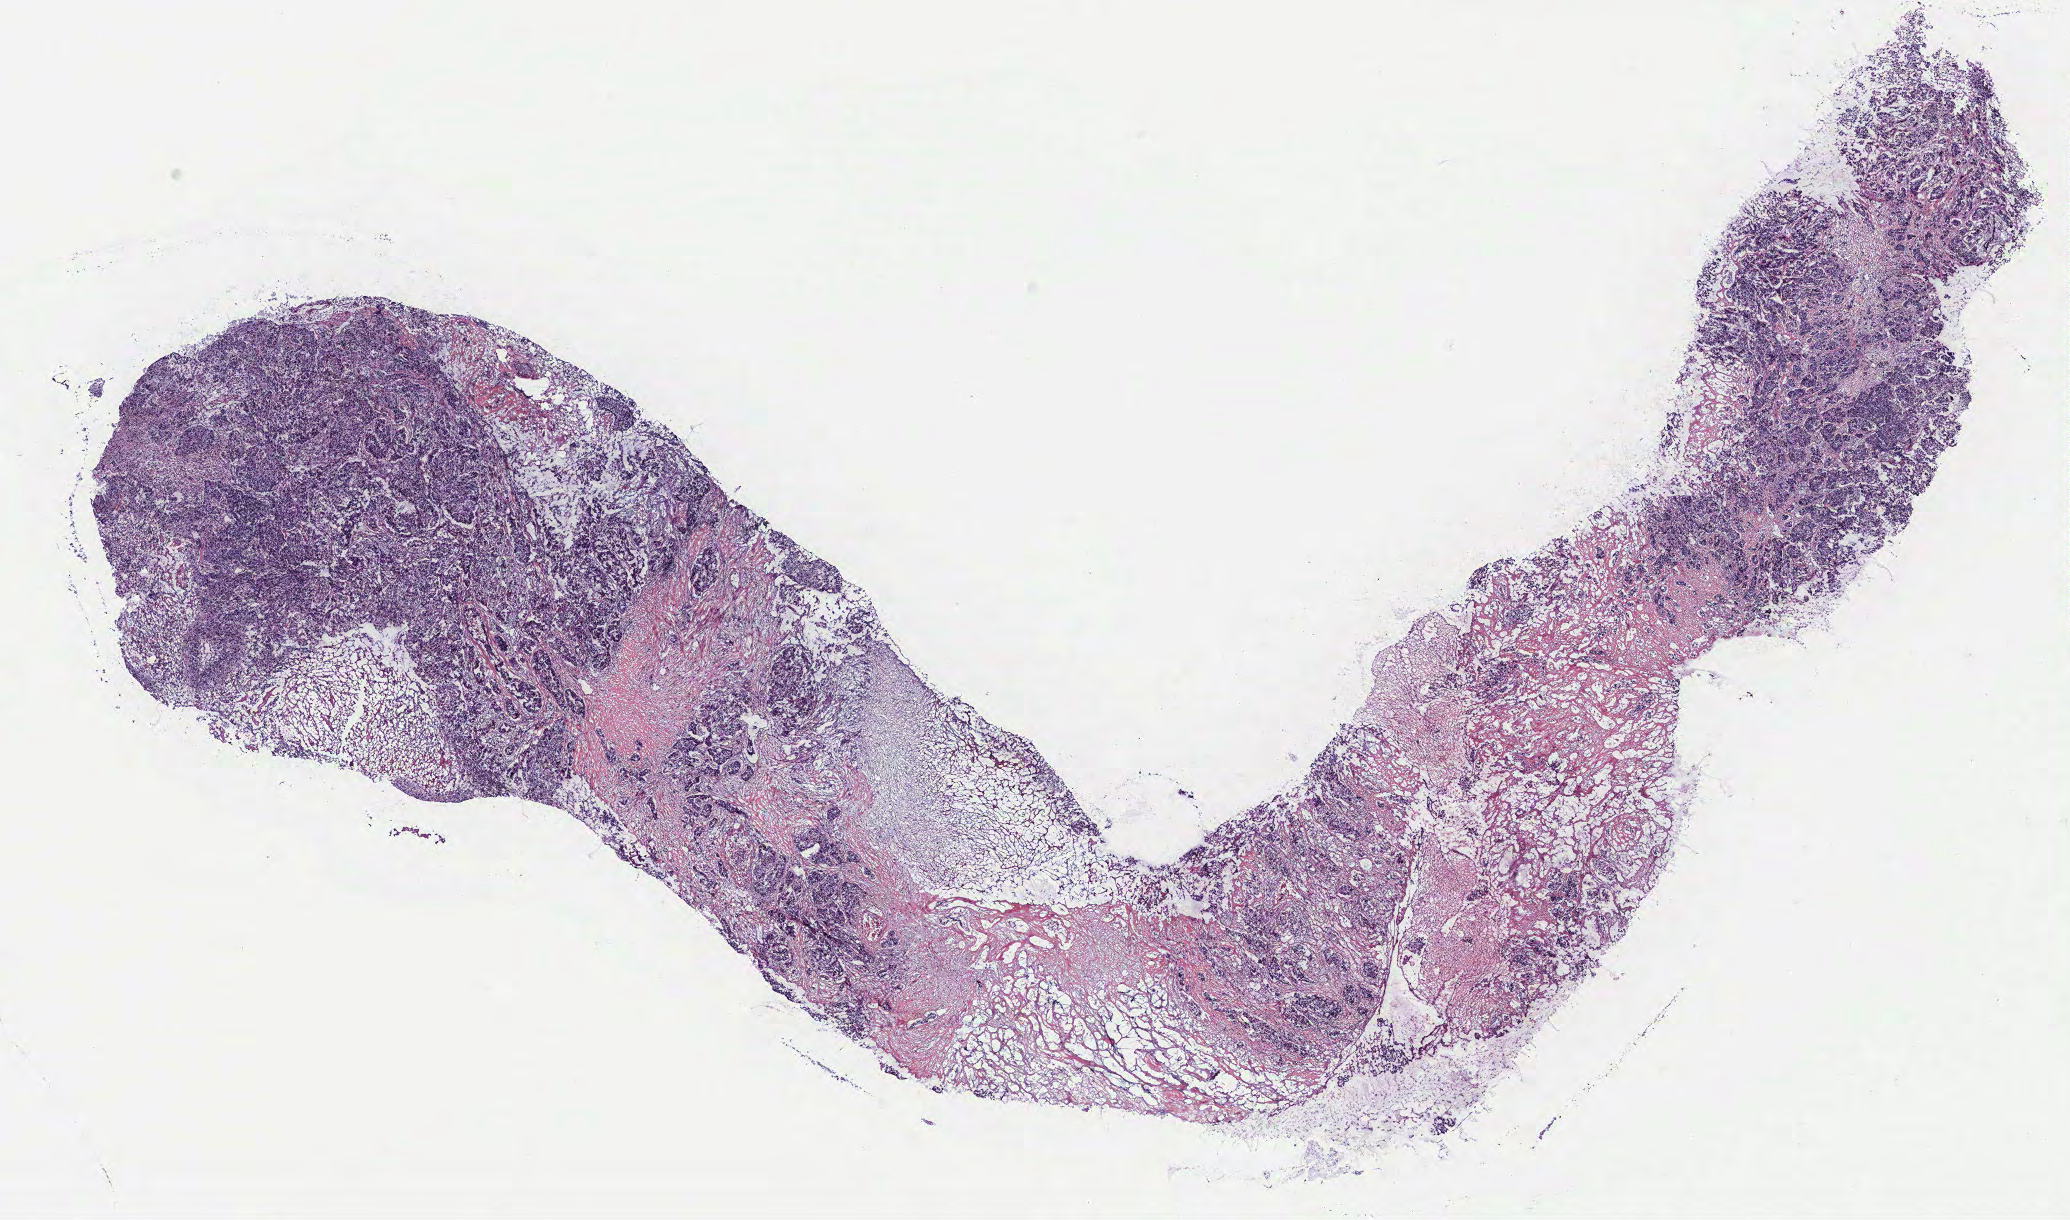
Whole-slide histology image, H&E, a low-resolution overview of the entire scanned area, about 16.6 x 9.8 mm (slide scanned at 40x), breast, tissue type not recorded. Female, 54 y/o.
Patient diagnosis: Infiltrating duct carcinoma, NOS.